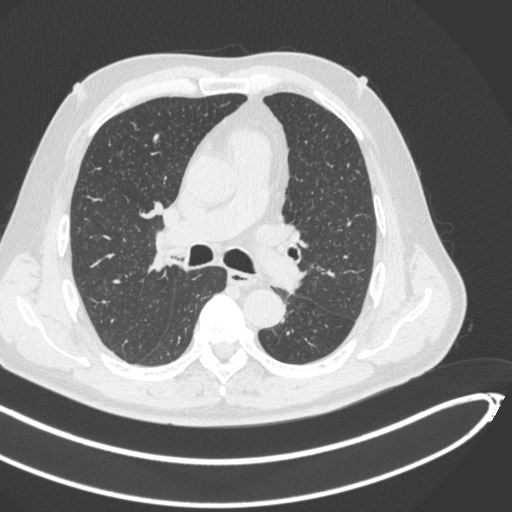
Chest CT, one axial slice. Slice 281 of 466 in the series (ordered by position). Reconstruction kernel B31f. 120 kVp. Lung window (W 1500 / L -600 HU). 512 × 512 image matrix. Patient: male, 64 years. From the clinical record (not read from this slice): clinical TNM (as recorded): T1c N0 M0.
Structures marked on this image (rectangle marked by the reading radiologist):
- lung tumour (recorded histology: squamous cell carcinoma): bounding box (x1, y1, x2, y2) in pixels: (253, 238, 305, 292)